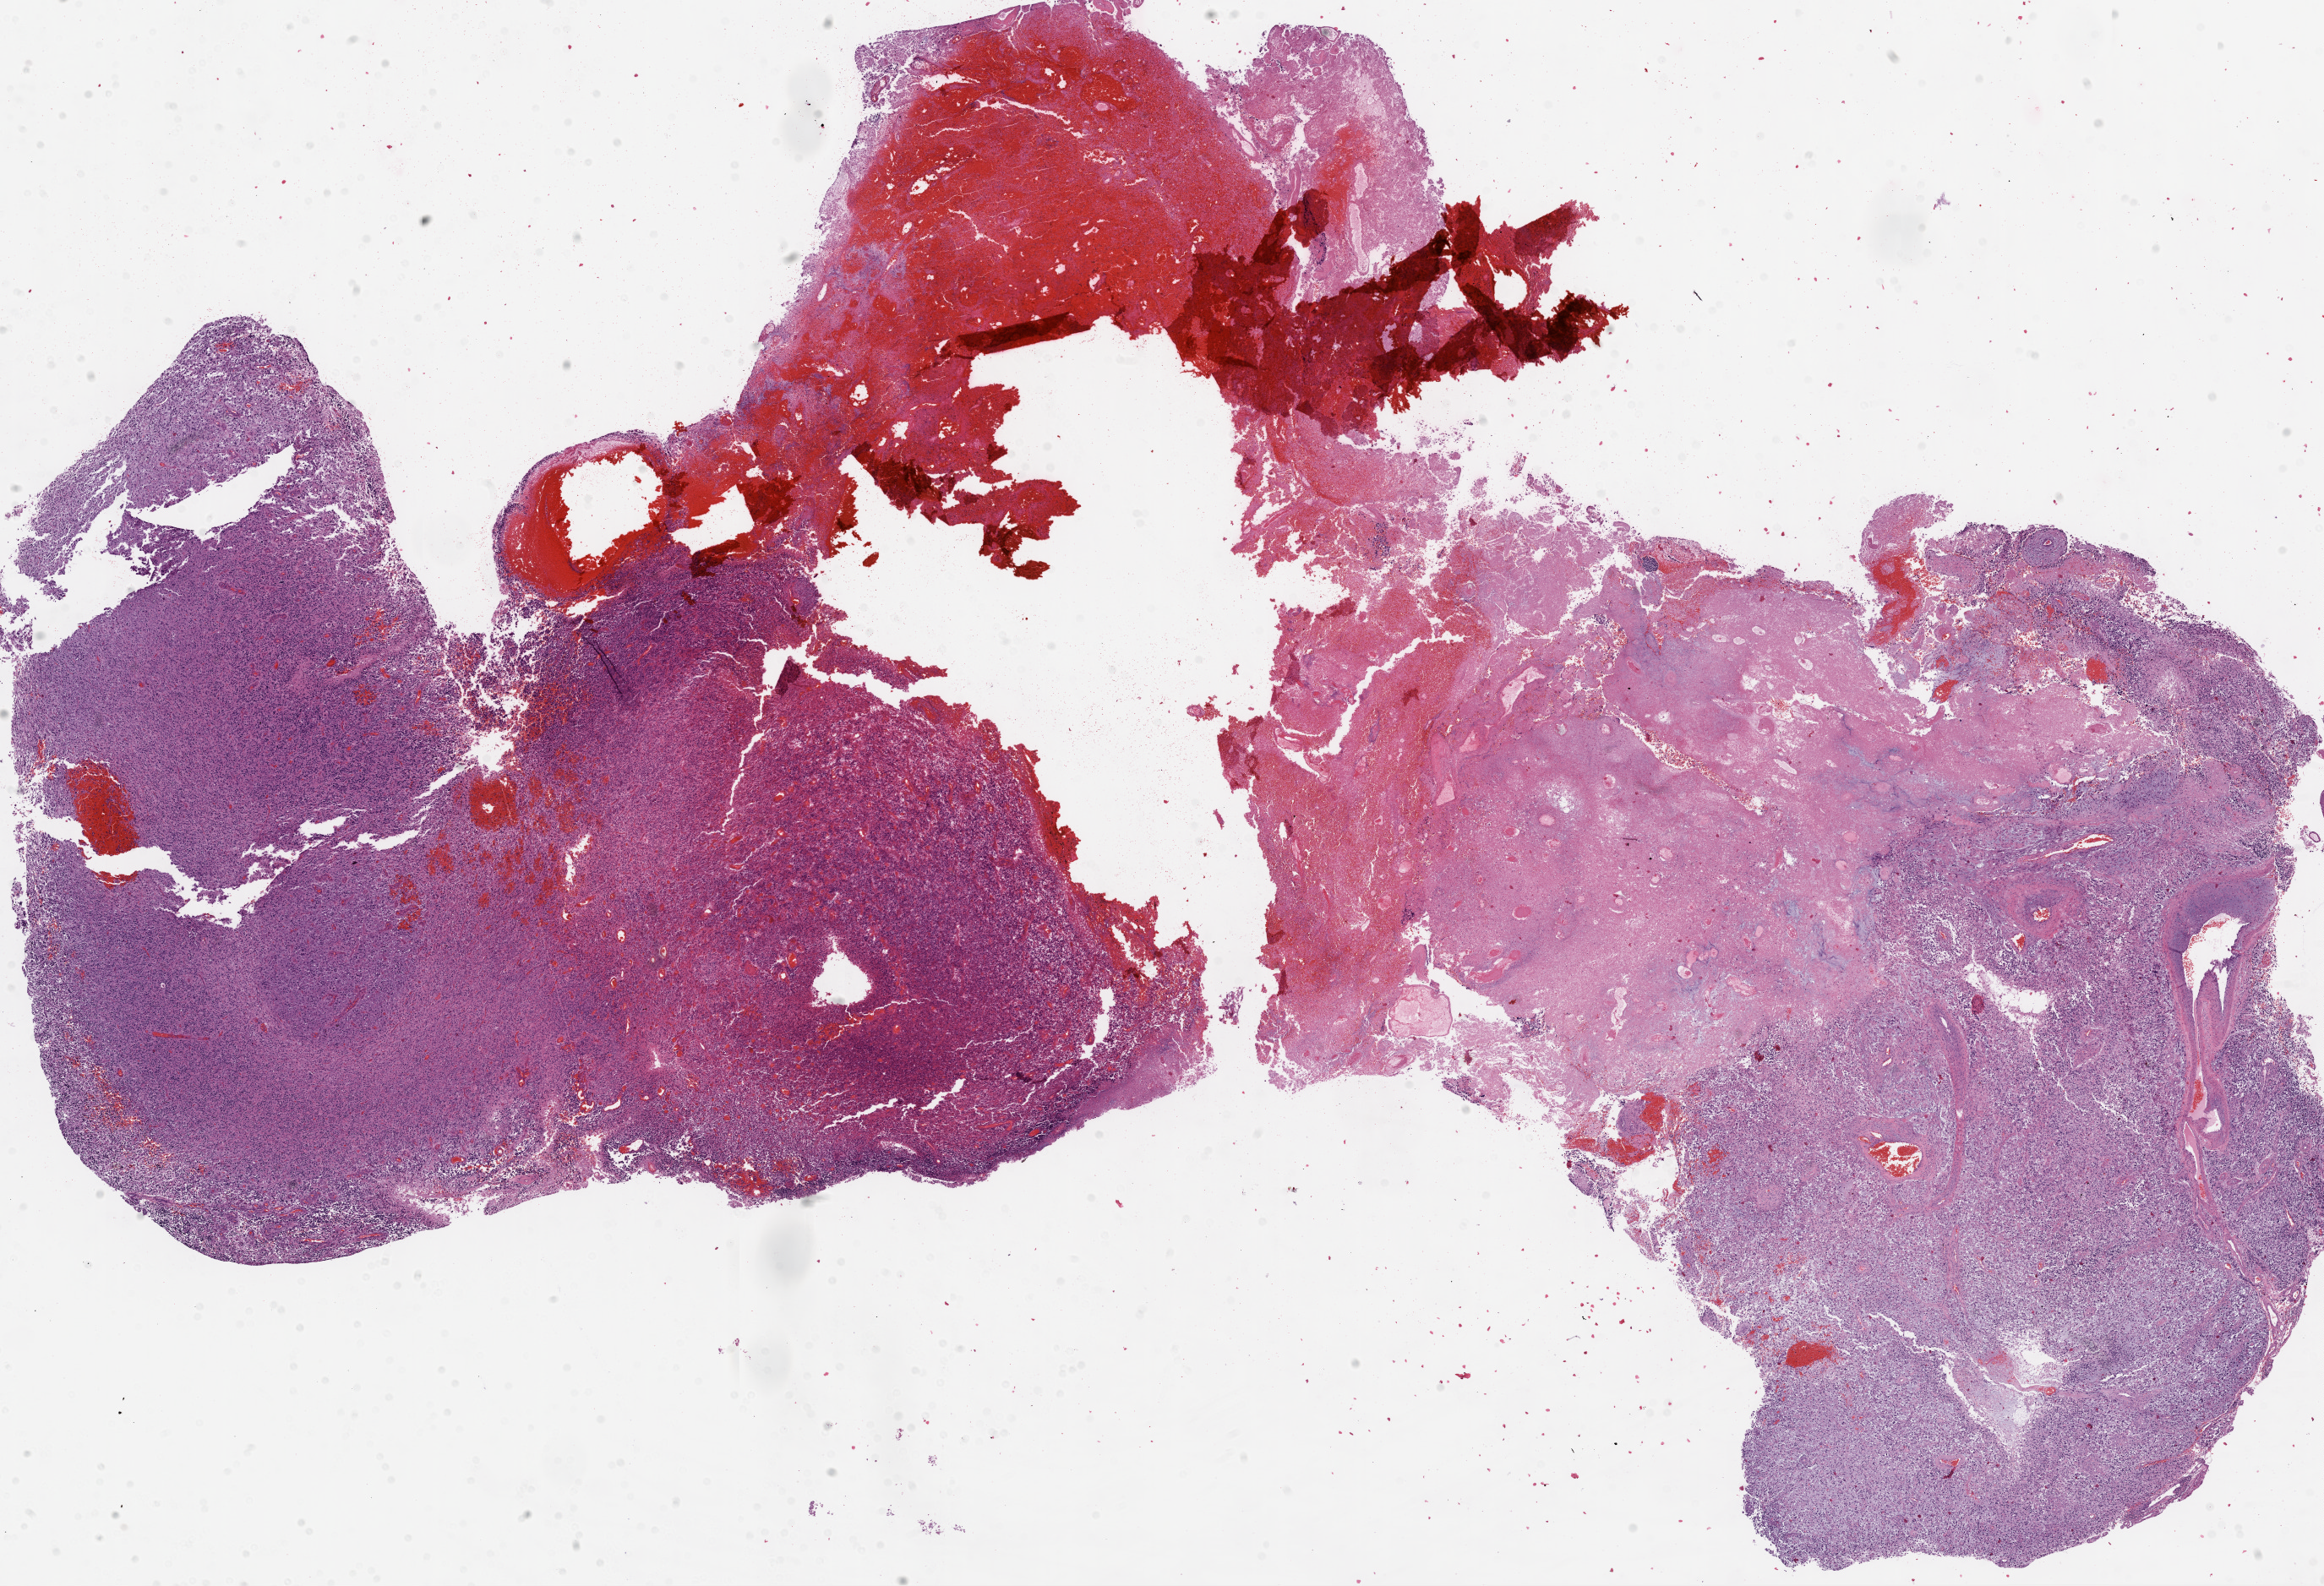
Whole-slide histology image, Hematoxylin and eosin (H&E) stained — low-resolution overview of the scanned area, about 22.1 x 15.1 mm (slide scanned at 20x); formalin-fixed paraffin-embedded (FFPE) diagnostic section; brain, primary tumour sample. Patient: female, age at initial diagnosis 78 years.
Diagnosis: Glioblastoma.